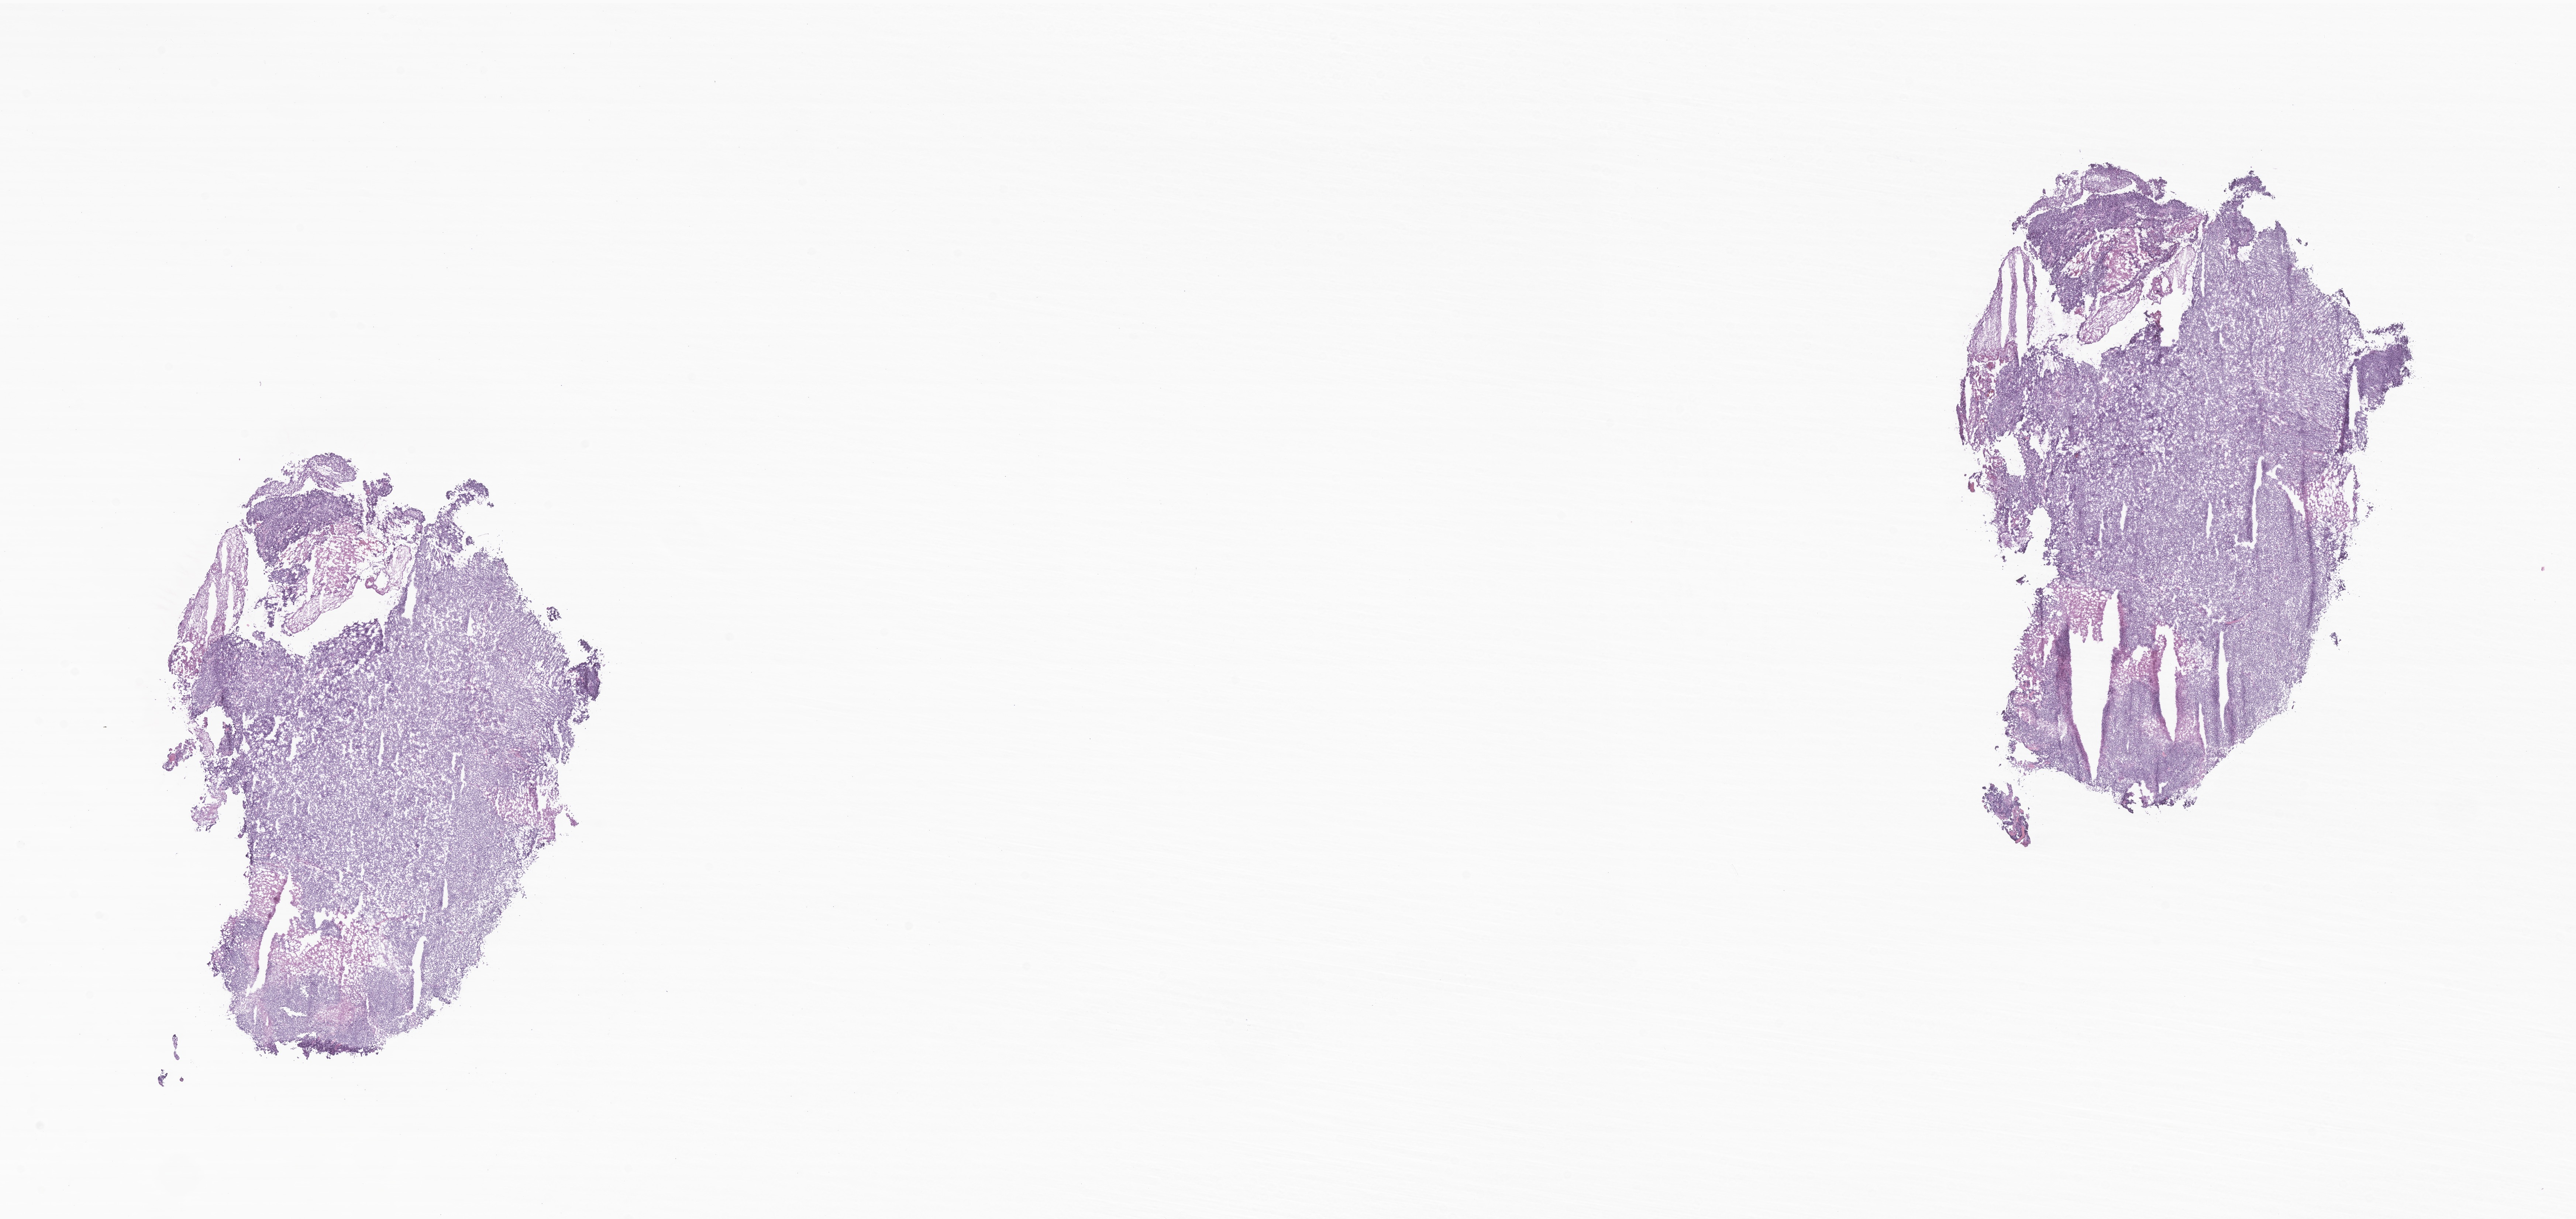
Digitized hematoxylin and eosin (H&E)-stained section of tumor tissue from the retroperitoneum — shown as a low-resolution overview of the whole scanned area (about 29.4 x 13.9 mm). Cryosection (OCT / tissue freezing medium). Female patient, age 207 months (17 years 3 months).
Diagnosis (ICD-O-3 morphology term): Rhabdomyosarcoma, NOS.